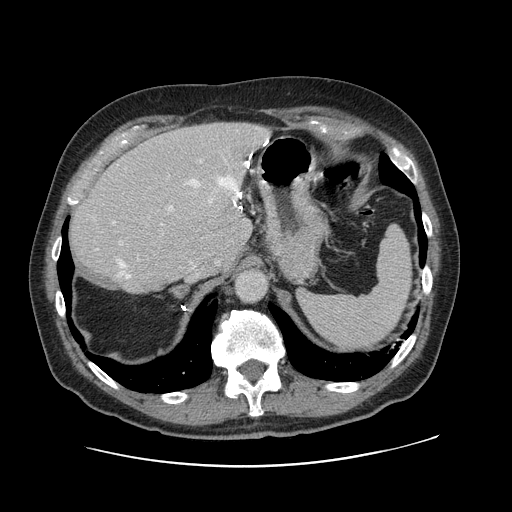
Contrast-enhanced abdominal CT, one axial slice. Slice 85 of 138 in the series (ordered by position). 120 kVp. Intravenous contrast given. Soft-tissue window (W 400 / L 40 HU). 2.5 mm slice thickness. 512 × 512 image matrix, field of view 402 × 402 mm. Male patient, age 71 years. From the clinical record (not read from this slice): diagnosis: colorectal cancer liver metastases, imaged before liver resection; multiple liver metastases: no; largest metastasis: 3.3 cm; chemotherapy before resection: no.
Outlined on this slice (manually delineated by an expert):
- hepatic veins: box from (x=117, y=154) to (x=252, y=279) px
- liver: (x=69, y=123)–(x=268, y=293)
- planned liver remnant (the part of the liver to remain after resection): (x=69, y=151)–(x=240, y=294)
- portal vein (with intrahepatic branches): (x=118, y=161)–(x=202, y=245)
- liver metastasis: (x=221, y=195)–(x=236, y=212)